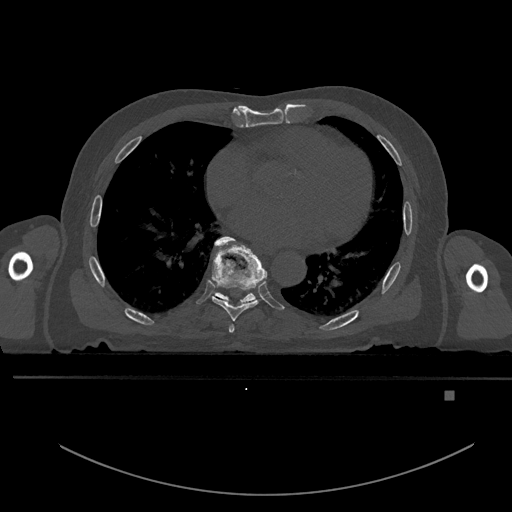
CT including the spine, one axial slice. Position 238 of 969 along the scan axis. Bone window (W 1800 / L 400 HU). 0.5 mm slice thickness. 512 × 512 image matrix, field of view 456 × 456 mm. Patient: male, 82 years. From the clinical record (not read from this slice): primary cancer: prostate.
Annotated regions visible in this slice (semi-automatically segmented with operator editing):
- T6 vertebra: bounding box (x1, y1, x2, y2) in pixels: (228, 324, 235, 333)
- T7 vertebra: (211, 236, 267, 321)
- T8 vertebra: (211, 240, 256, 304)